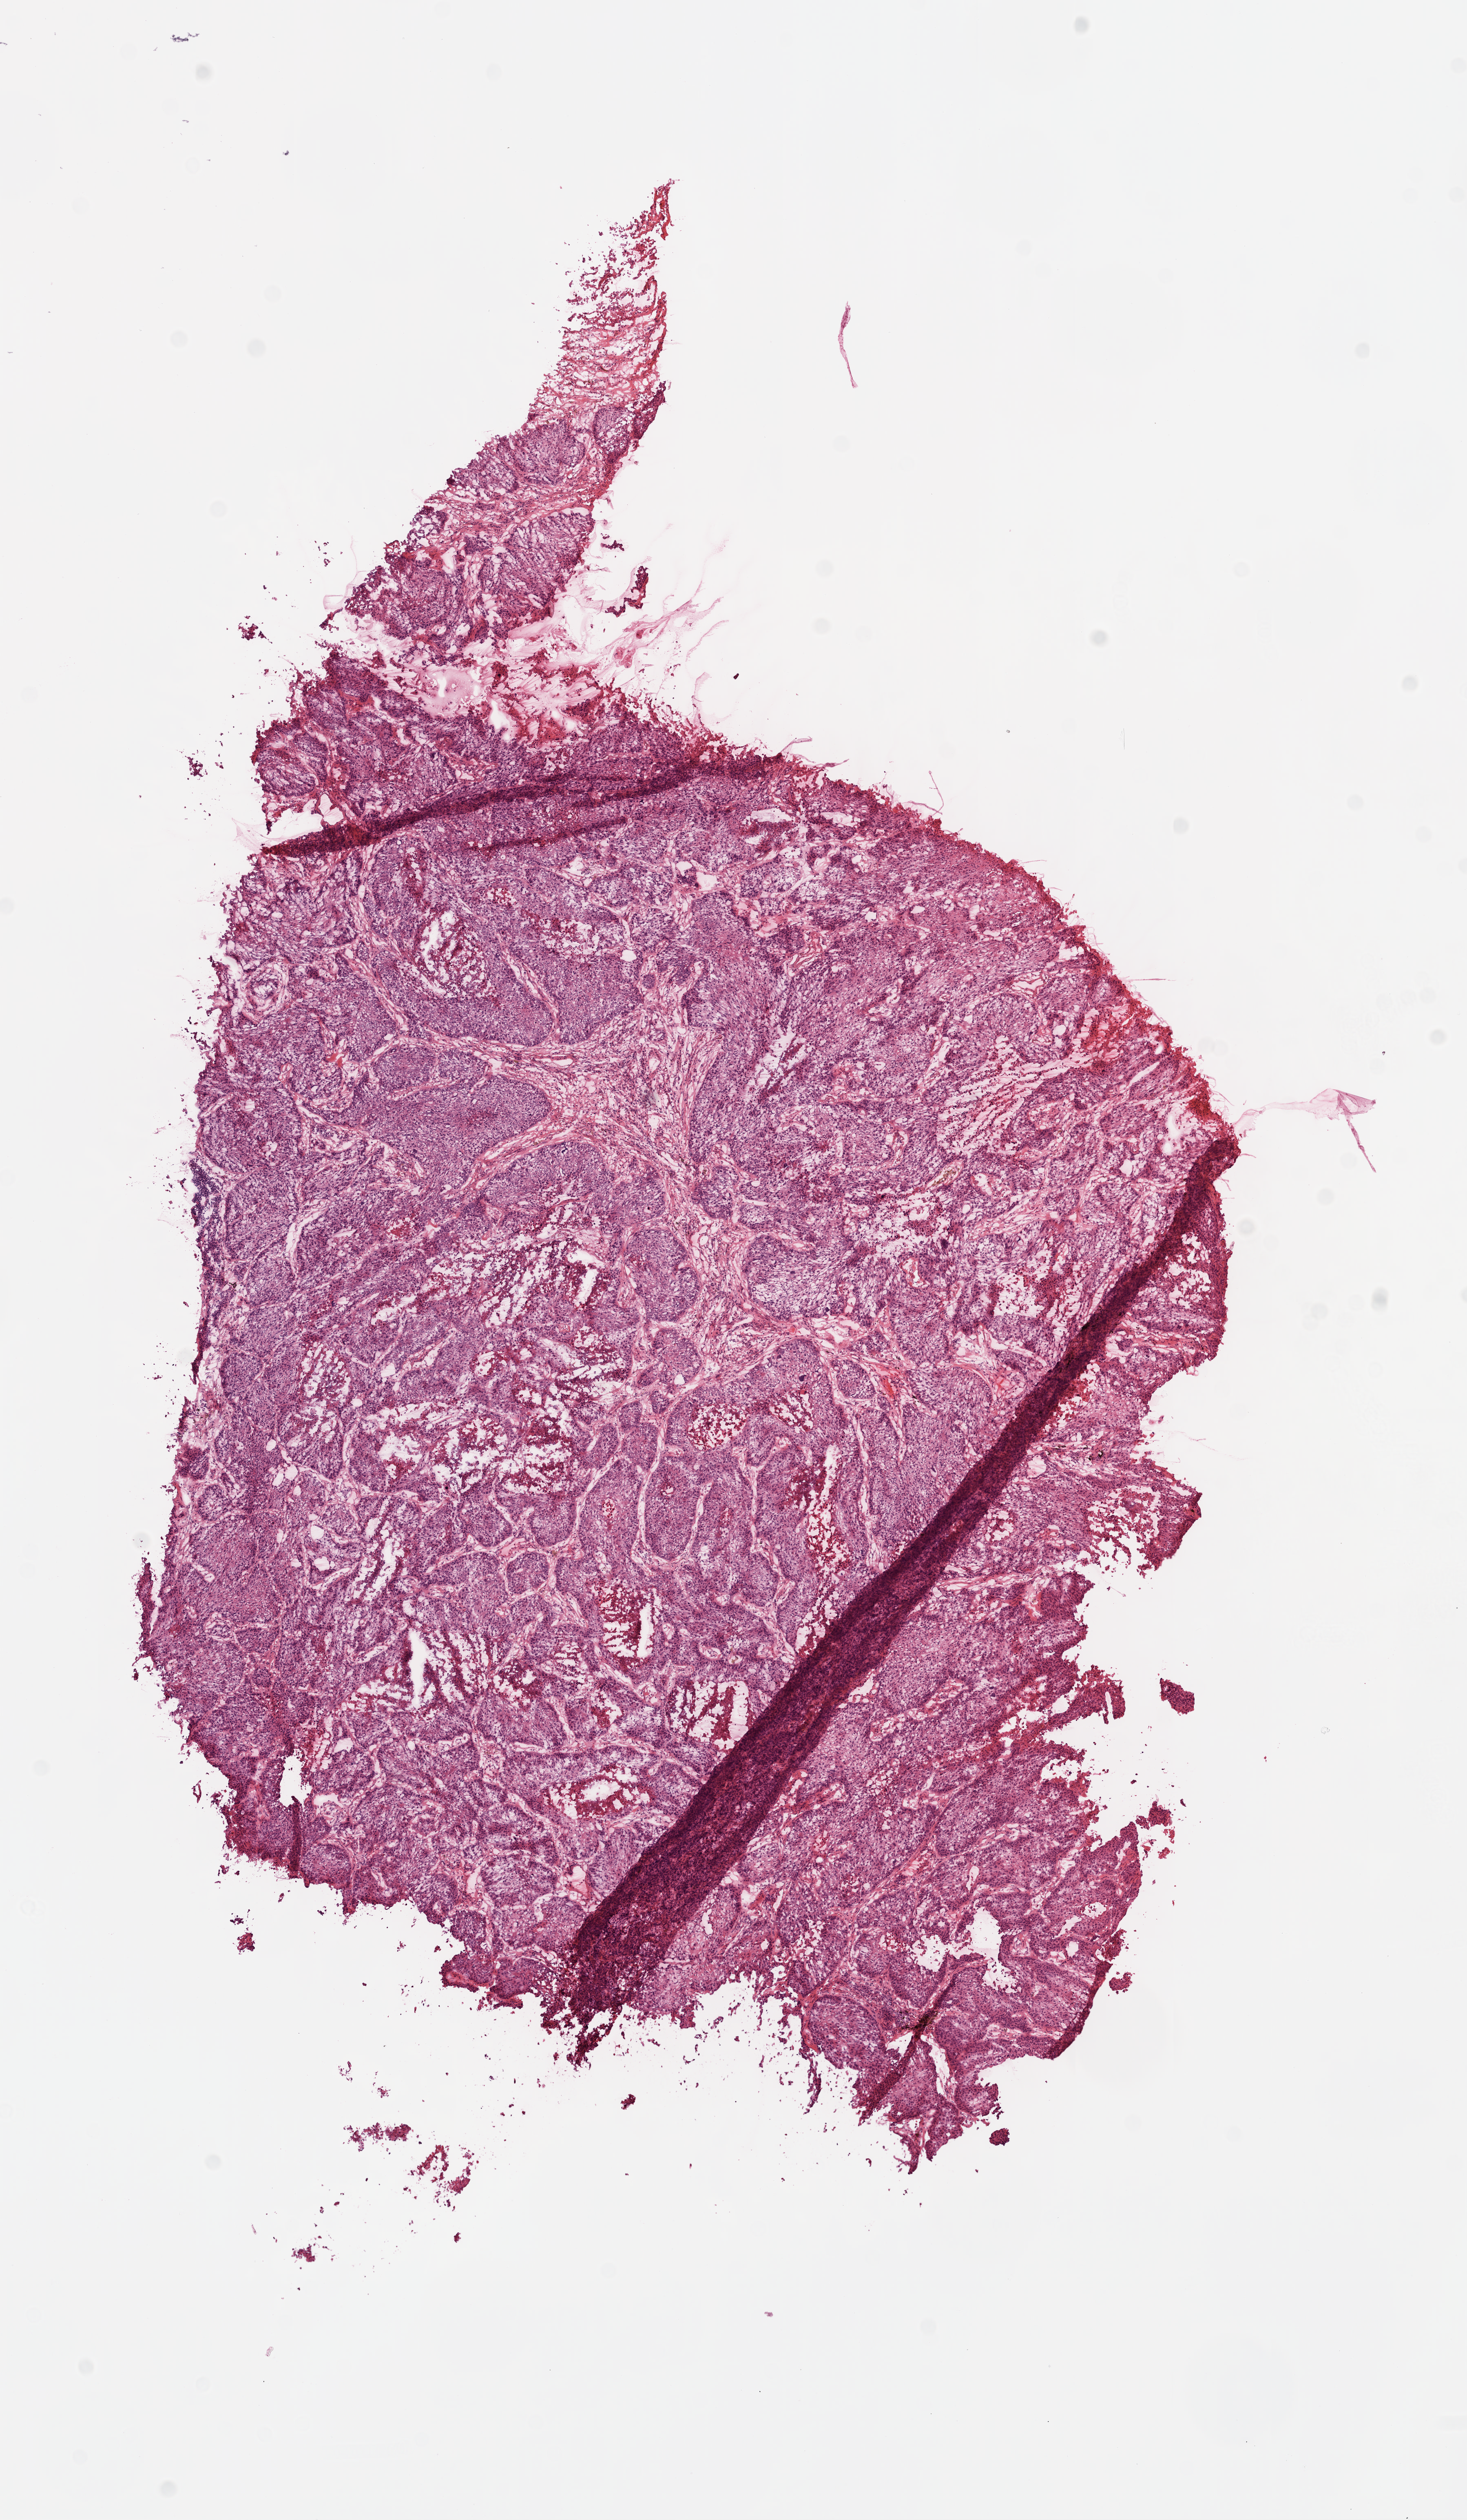
Digitized H&E tissue section (whole slide), whole scanned area (about 7.3 x 12.5 mm, acquisition: 20x scan) shown as a low-resolution overview; frozen section; sample: primary tumour, lung. Male, age 57 years at initial diagnosis. Slide review estimates, as recorded: tumour nuclei 95%, necrosis 0%.
• pathologic diagnosis: Squamous cell carcinoma, NOS (lower lobe, lung)
• AJCC pathologic stage: IIB
• TNM: T2 N1 M0